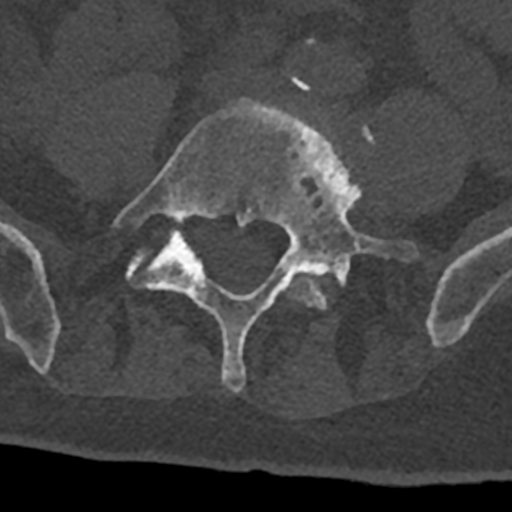
CT including the spine, one axial slice. Position 207 of 797 along the scan axis. Reconstruction kernel Br40s/3. 120 kVp. Bone window (W 1800 / L 400 HU). 0.5 mm slice thickness. 512 × 512 image matrix. Male patient, age 74 years. Case-level facts recorded for this patient, not image findings: primary cancer: renal; vertebrae with lytic lesions (as recorded): T10, L1, L2, L3, L4, L5.
Annotated regions visible in this slice (semi-automatic segmentation, software-assisted and operator-edited):
- L4 vertebra: box from (x=284, y=76) to (x=375, y=310) px
- L5 vertebra: (x=112, y=98)–(x=416, y=391)